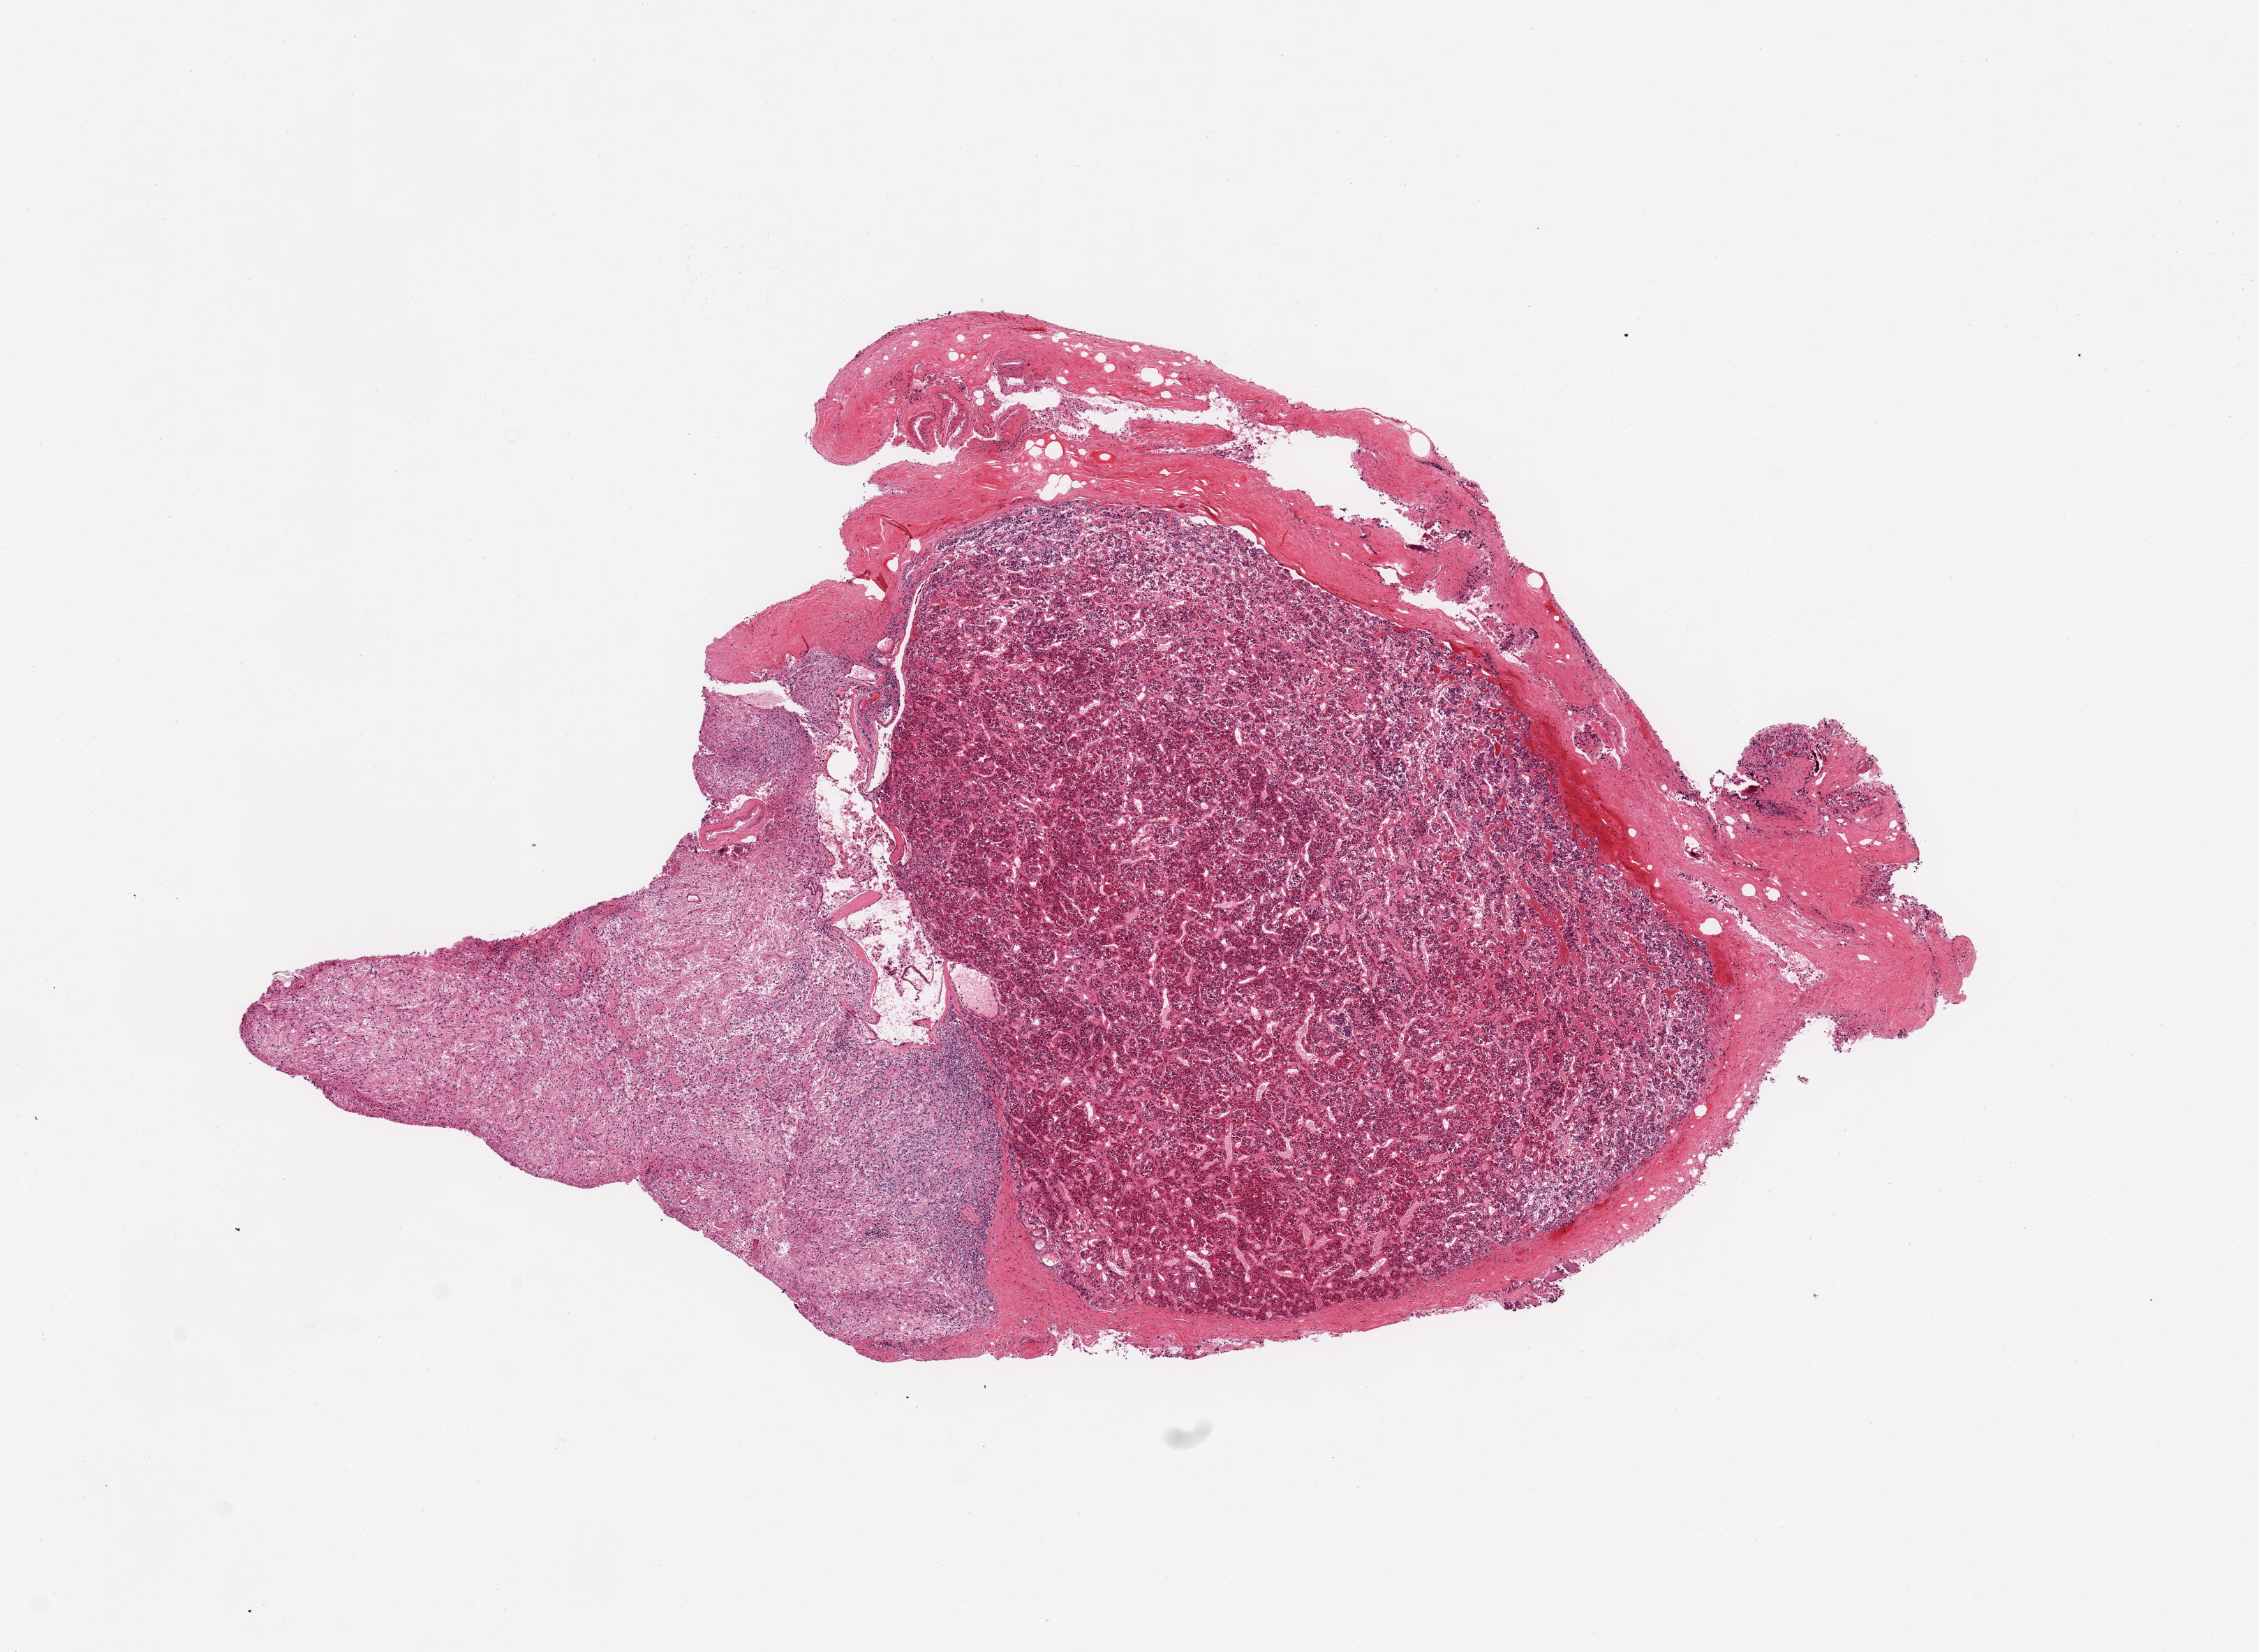
Haematoxylin and eosin whole-slide image, brightfield, whole scanned area (about 12.8 x 9.4 mm) shown as a low-resolution overview; PAXgene-fixed, paraffin-embedded tissue; target tissue: pituitary; tissue donor sample. Donor: male.
Review note (as recorded): 1 piece, ~50% each adenohypophysis and neurohypophysis, ~4x4mm.